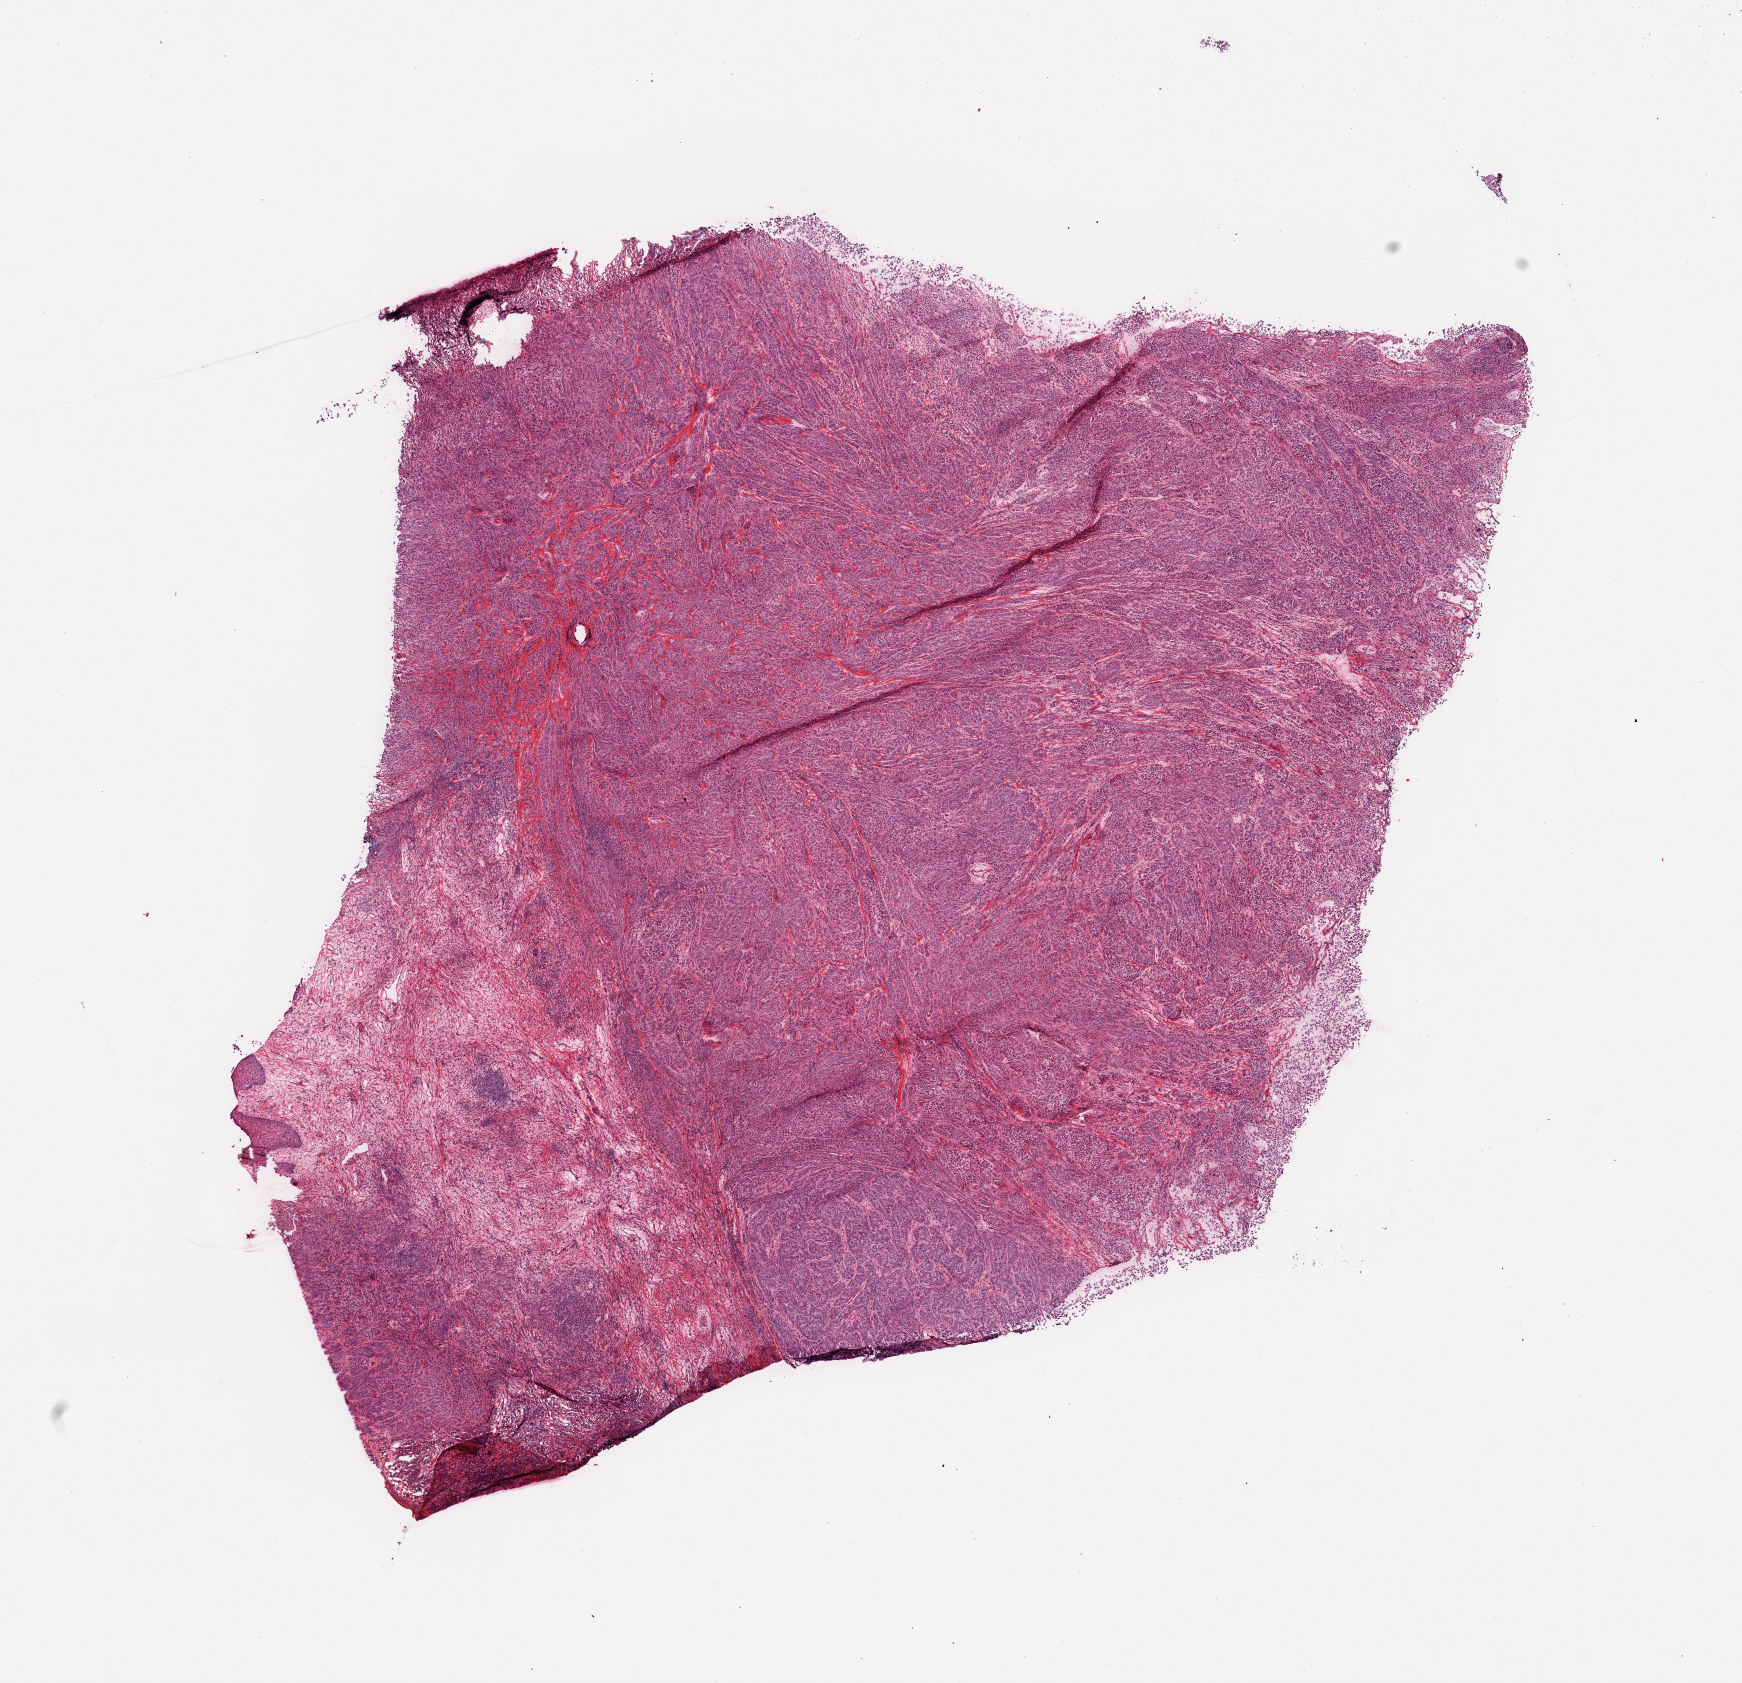
Hematoxylin and eosin (H&E) stained whole-slide image, a low-resolution overview of the entire scanned area, about 13.8 x 13.3 mm (slide scanned at 20x), melanoma tumour tissue; sampled site not recorded. 51-year-old female patient.
• primary tumour site (as recorded): extremities
• patient diagnosis (cohort enrolment): cutaneous melanoma (skin)